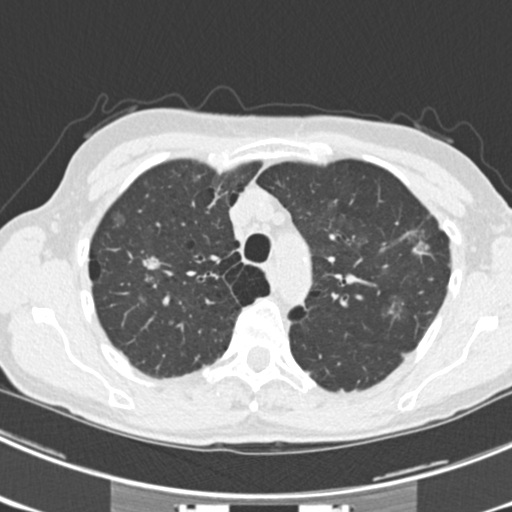
Low-dose screening chest CT, one axial slice. Position 170 of 225 along the scan axis. Lung window (W 1500 / L -600 HU). 2 mm slice thickness. 512 × 512 image matrix, field of view 302 × 302 mm.
Annotated regions visible in this slice (outlined manually by an expert reader):
- lesion 3 (tumor, upper lobe of right lung): bounding box (x1, y1, x2, y2) in pixels: (143, 256, 161, 269)